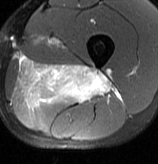
MRI of an extremity soft-tissue mass, one axial slice. Position 37 of 70 along the scan axis. T2-weighted fat-saturated. MR volume resampled by the dataset authors to the PET/CT grid (not the native acquisition matrix). 3.27 mm slice thickness. 158 × 164 image matrix. Male patient. From the clinical record (not read from this slice): histological type: extraskeletal osteosarcoma; grade: high; site of the primary tumour: left adductur.
Annotated regions visible in this slice (expert contour drawn on MRI and transferred to this co-registered scan by the dataset authors):
- gross tumour volume (mass): bounding box (x1, y1, x2, y2) in pixels: (17, 55, 121, 109)